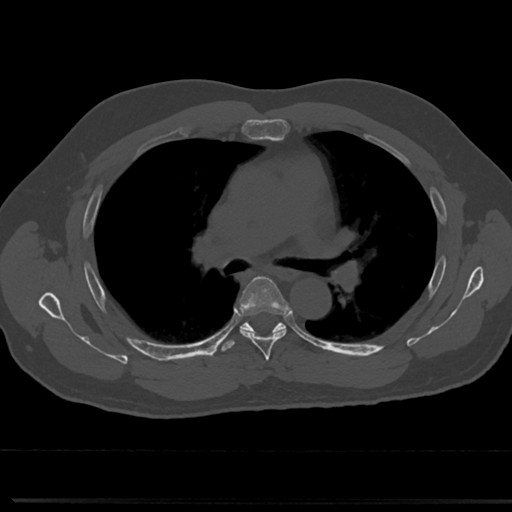
CT including the spine, one axial slice. Position 484 of 817 along the scan axis. Reconstruction kernel Br40s/3. Bone window (W 1800 / L 400 HU). 0.5 mm slice thickness. 512 × 512 image matrix. Male patient, age 61 years. Case-level facts recorded for this patient, not image findings: primary cancer: prostate.
Structures marked on this image (semi-automatically segmented with operator editing):
- T4 vertebra: box from (x=266, y=367) to (x=272, y=374) px
- T5 vertebra: (x=237, y=278)–(x=289, y=354)
- T6 vertebra: (x=242, y=327)–(x=285, y=333)